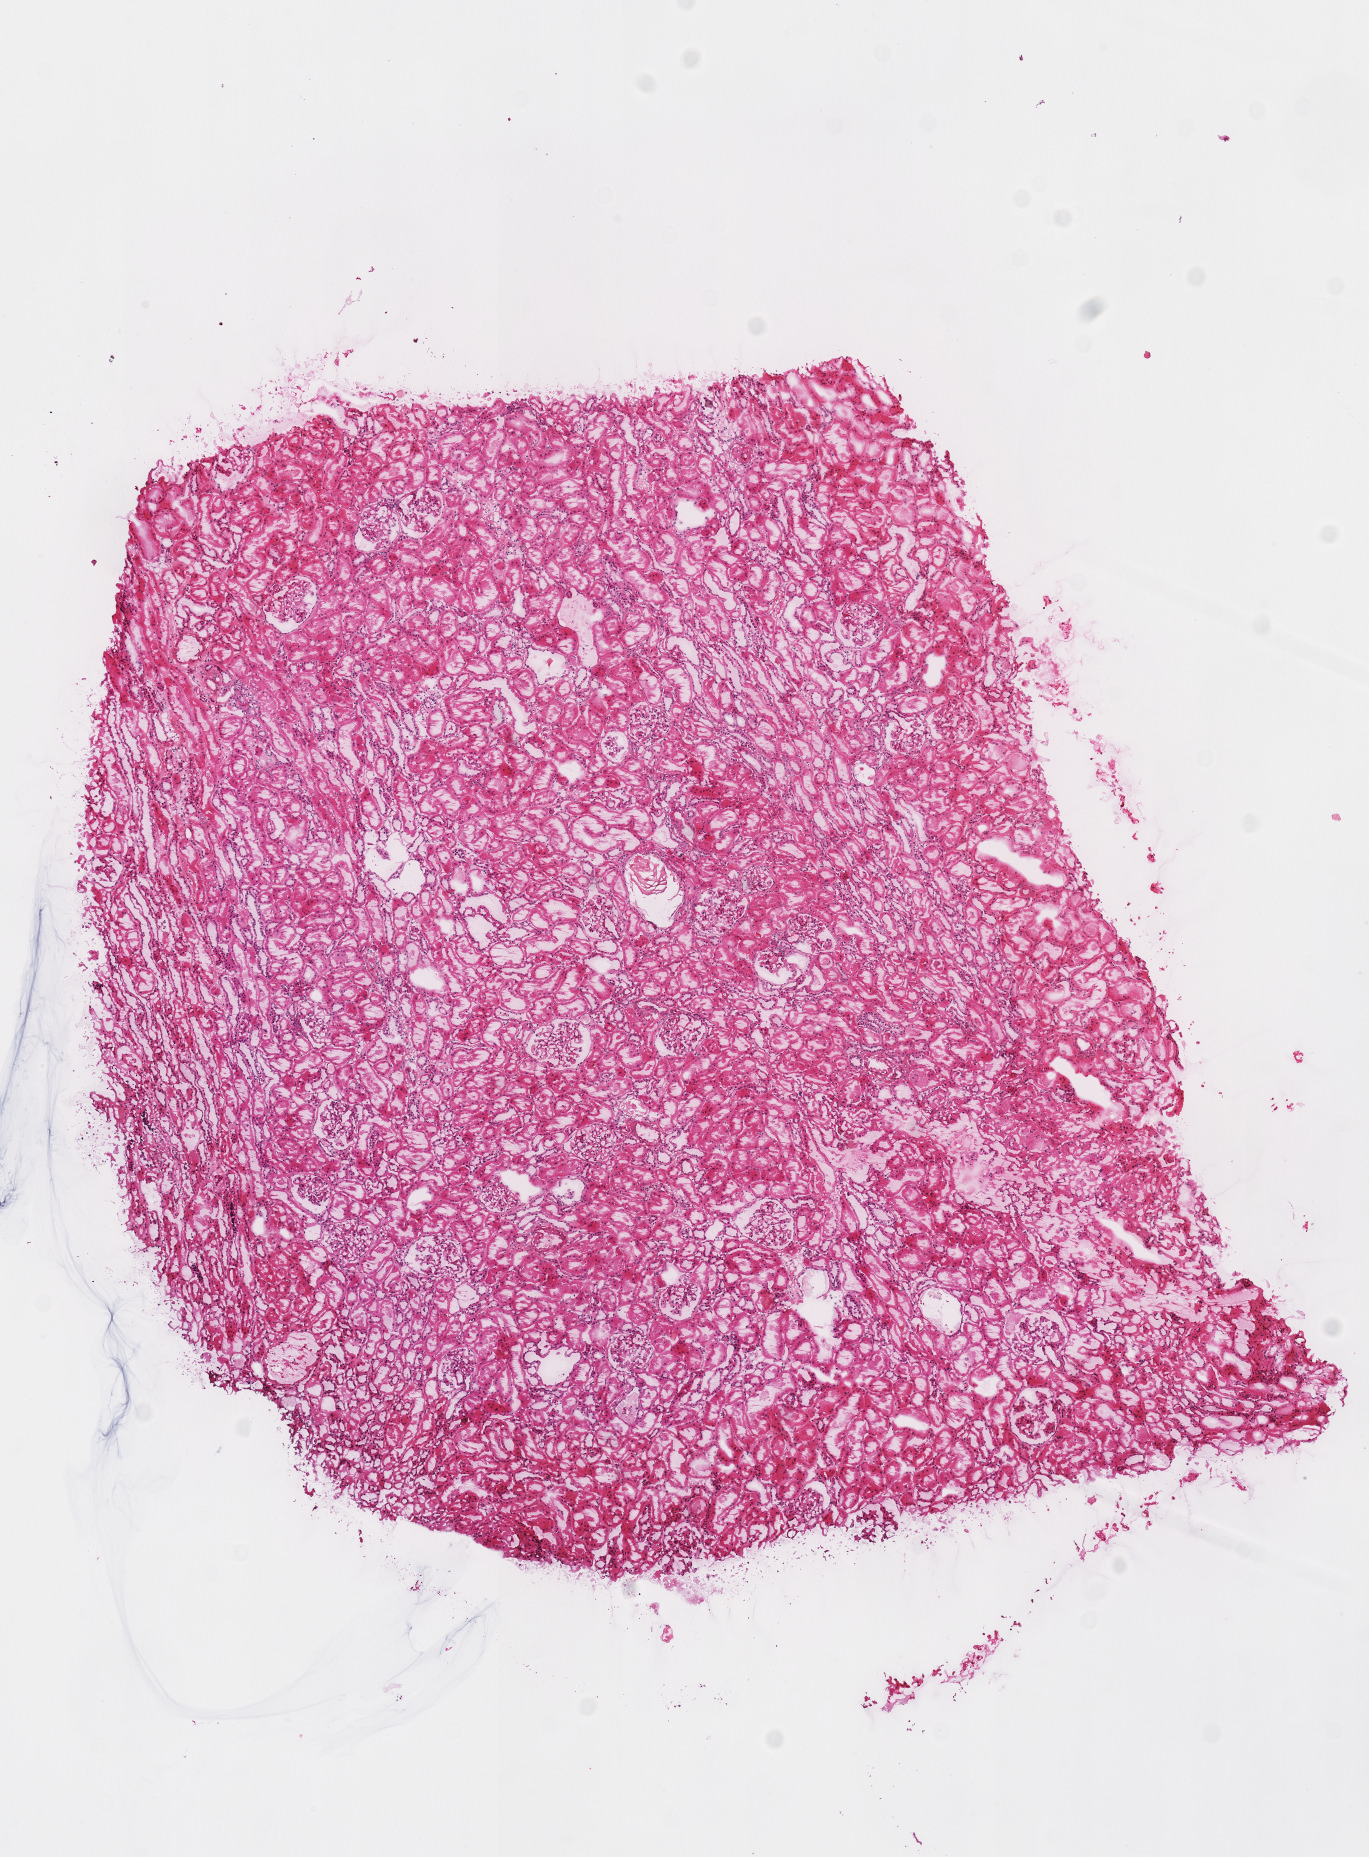
Digitized H&E-stained tissue section (whole slide), whole scanned area (about 5.4 x 7.3 mm) shown as a low-resolution overview; frozen section from the top of the tissue portion; kidney, solid tissue normal (non-tumour tissue) sample. Patient: male, age at initial diagnosis 58 years.
• this section: solid tissue normal sample (biorepository sample class)
• patient diagnosis: Renal cell carcinoma, chromophobe type